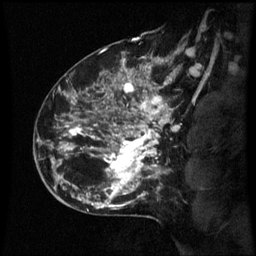
Breast MRI (dynamic contrast-enhanced), one sagittal slice; position 44 of 60 along the scan axis; dynamic contrast-enhanced series, image 2 of 3 at this slice position (ordered by acquisition); 1.5 T; TE 4.2 ms, TR 8.9 ms; 256 × 256 image matrix. Patient: female, 42 years. From the clinical record (not read from this slice): setting: breast cancer imaged before/during neoadjuvant chemotherapy; receptor status: HER2-positive.
Outlined on this slice (semi-automatically segmented with operator editing):
- analysis volume of interest (the breast-tissue region the enhancement analysis was run in; not a lesion): bounding box [x1, y1, x2, y2] px = [66, 82, 173, 193]
- tumour enhancement mask (voxels above the 70 % enhancement threshold inside the analysis volume of interest): [66, 82, 173, 193]